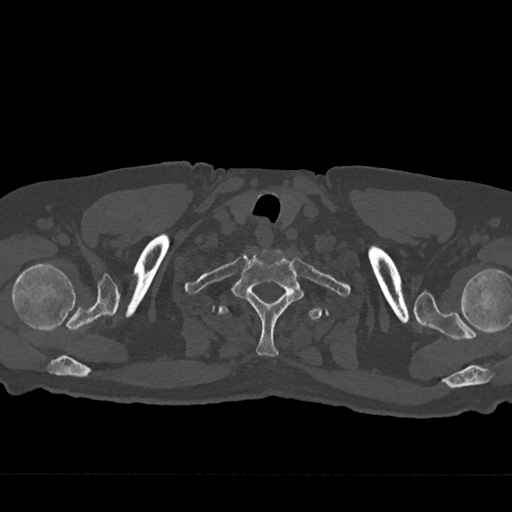
CT including the spine, one axial slice. Slice 655 of 797 in the series (ordered by position). 120 kVp. Bone window (W 1800 / L 400 HU). 0.5 mm slice thickness. 512 × 512 image matrix. Male patient, age 75 years. Case-level facts recorded for this patient, not image findings: primary cancer: renal; vertebrae with lytic lesions (as recorded): T4.
Structures marked on this image (semi-automatic segmentation, software-assisted and operator-edited):
- T1 vertebra: box from (x=230, y=250) to (x=305, y=357) px
- T2 vertebra: (x=218, y=291)–(x=322, y=320)